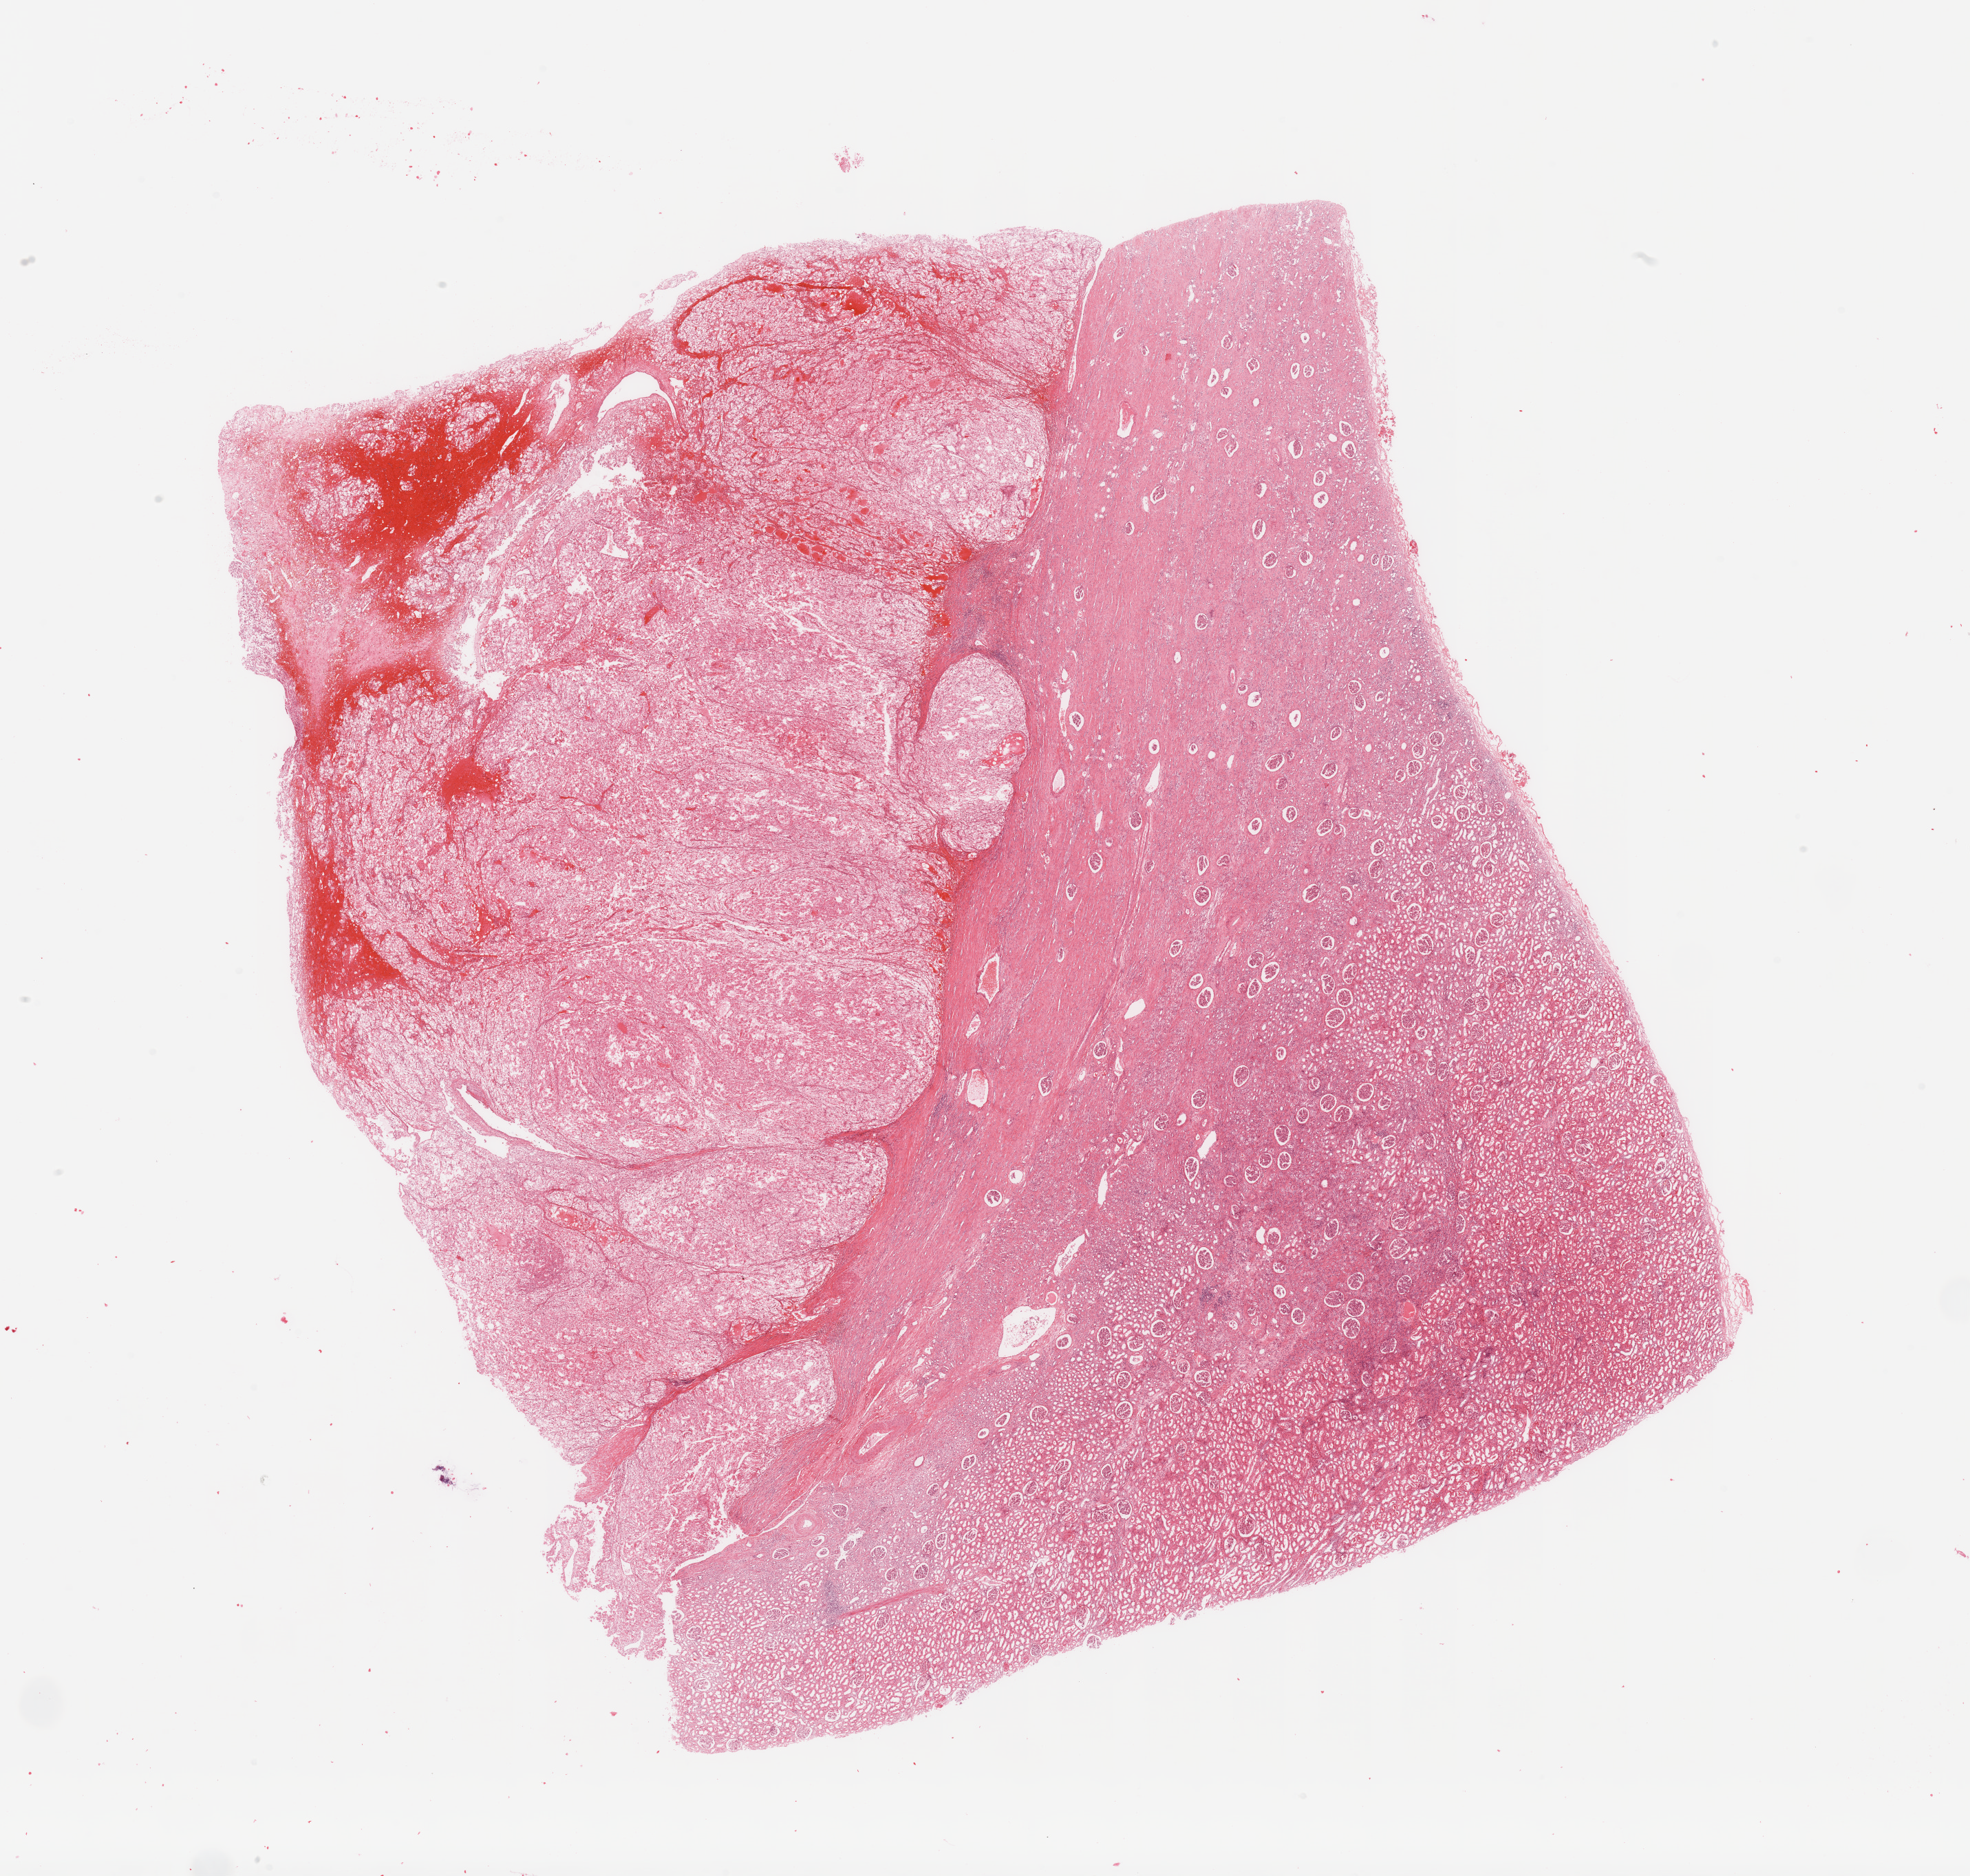
H&E whole-slide image, shown as a low-resolution overview of the whole scanned area (about 22.6 x 21.6 mm, acquisition: 20x scan). Tumour tissue sample, sampled site: kidney. Patient: male, age 47 years. Histologic grade: G3 (poorly differentiated). Pathologist review of this section (percent, as recorded): tumour nuclei 60%, necrosis 0%.
- histologic diagnosis: Renal cell carcinoma, NOS
- AJCC pathologic stage: I